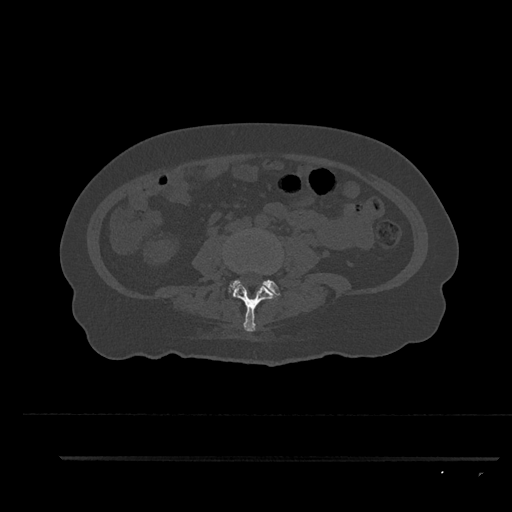
CT including the spine, one axial slice; position 58 of 797 along the scan axis; 120 kVp; bone window (W 1800 / L 400 HU); 0.5 mm slice thickness; 512 × 512 image matrix, field of view 408 × 408 mm. Female patient, age 44 years. From the clinical record (not read from this slice): primary cancer: renal.
Outlined on this slice (semi-automatically segmented with operator editing):
- L3 vertebra: bounding box (x1, y1, x2, y2) in pixels: (233, 282, 280, 331)
- L4 vertebra: (228, 280, 281, 296)